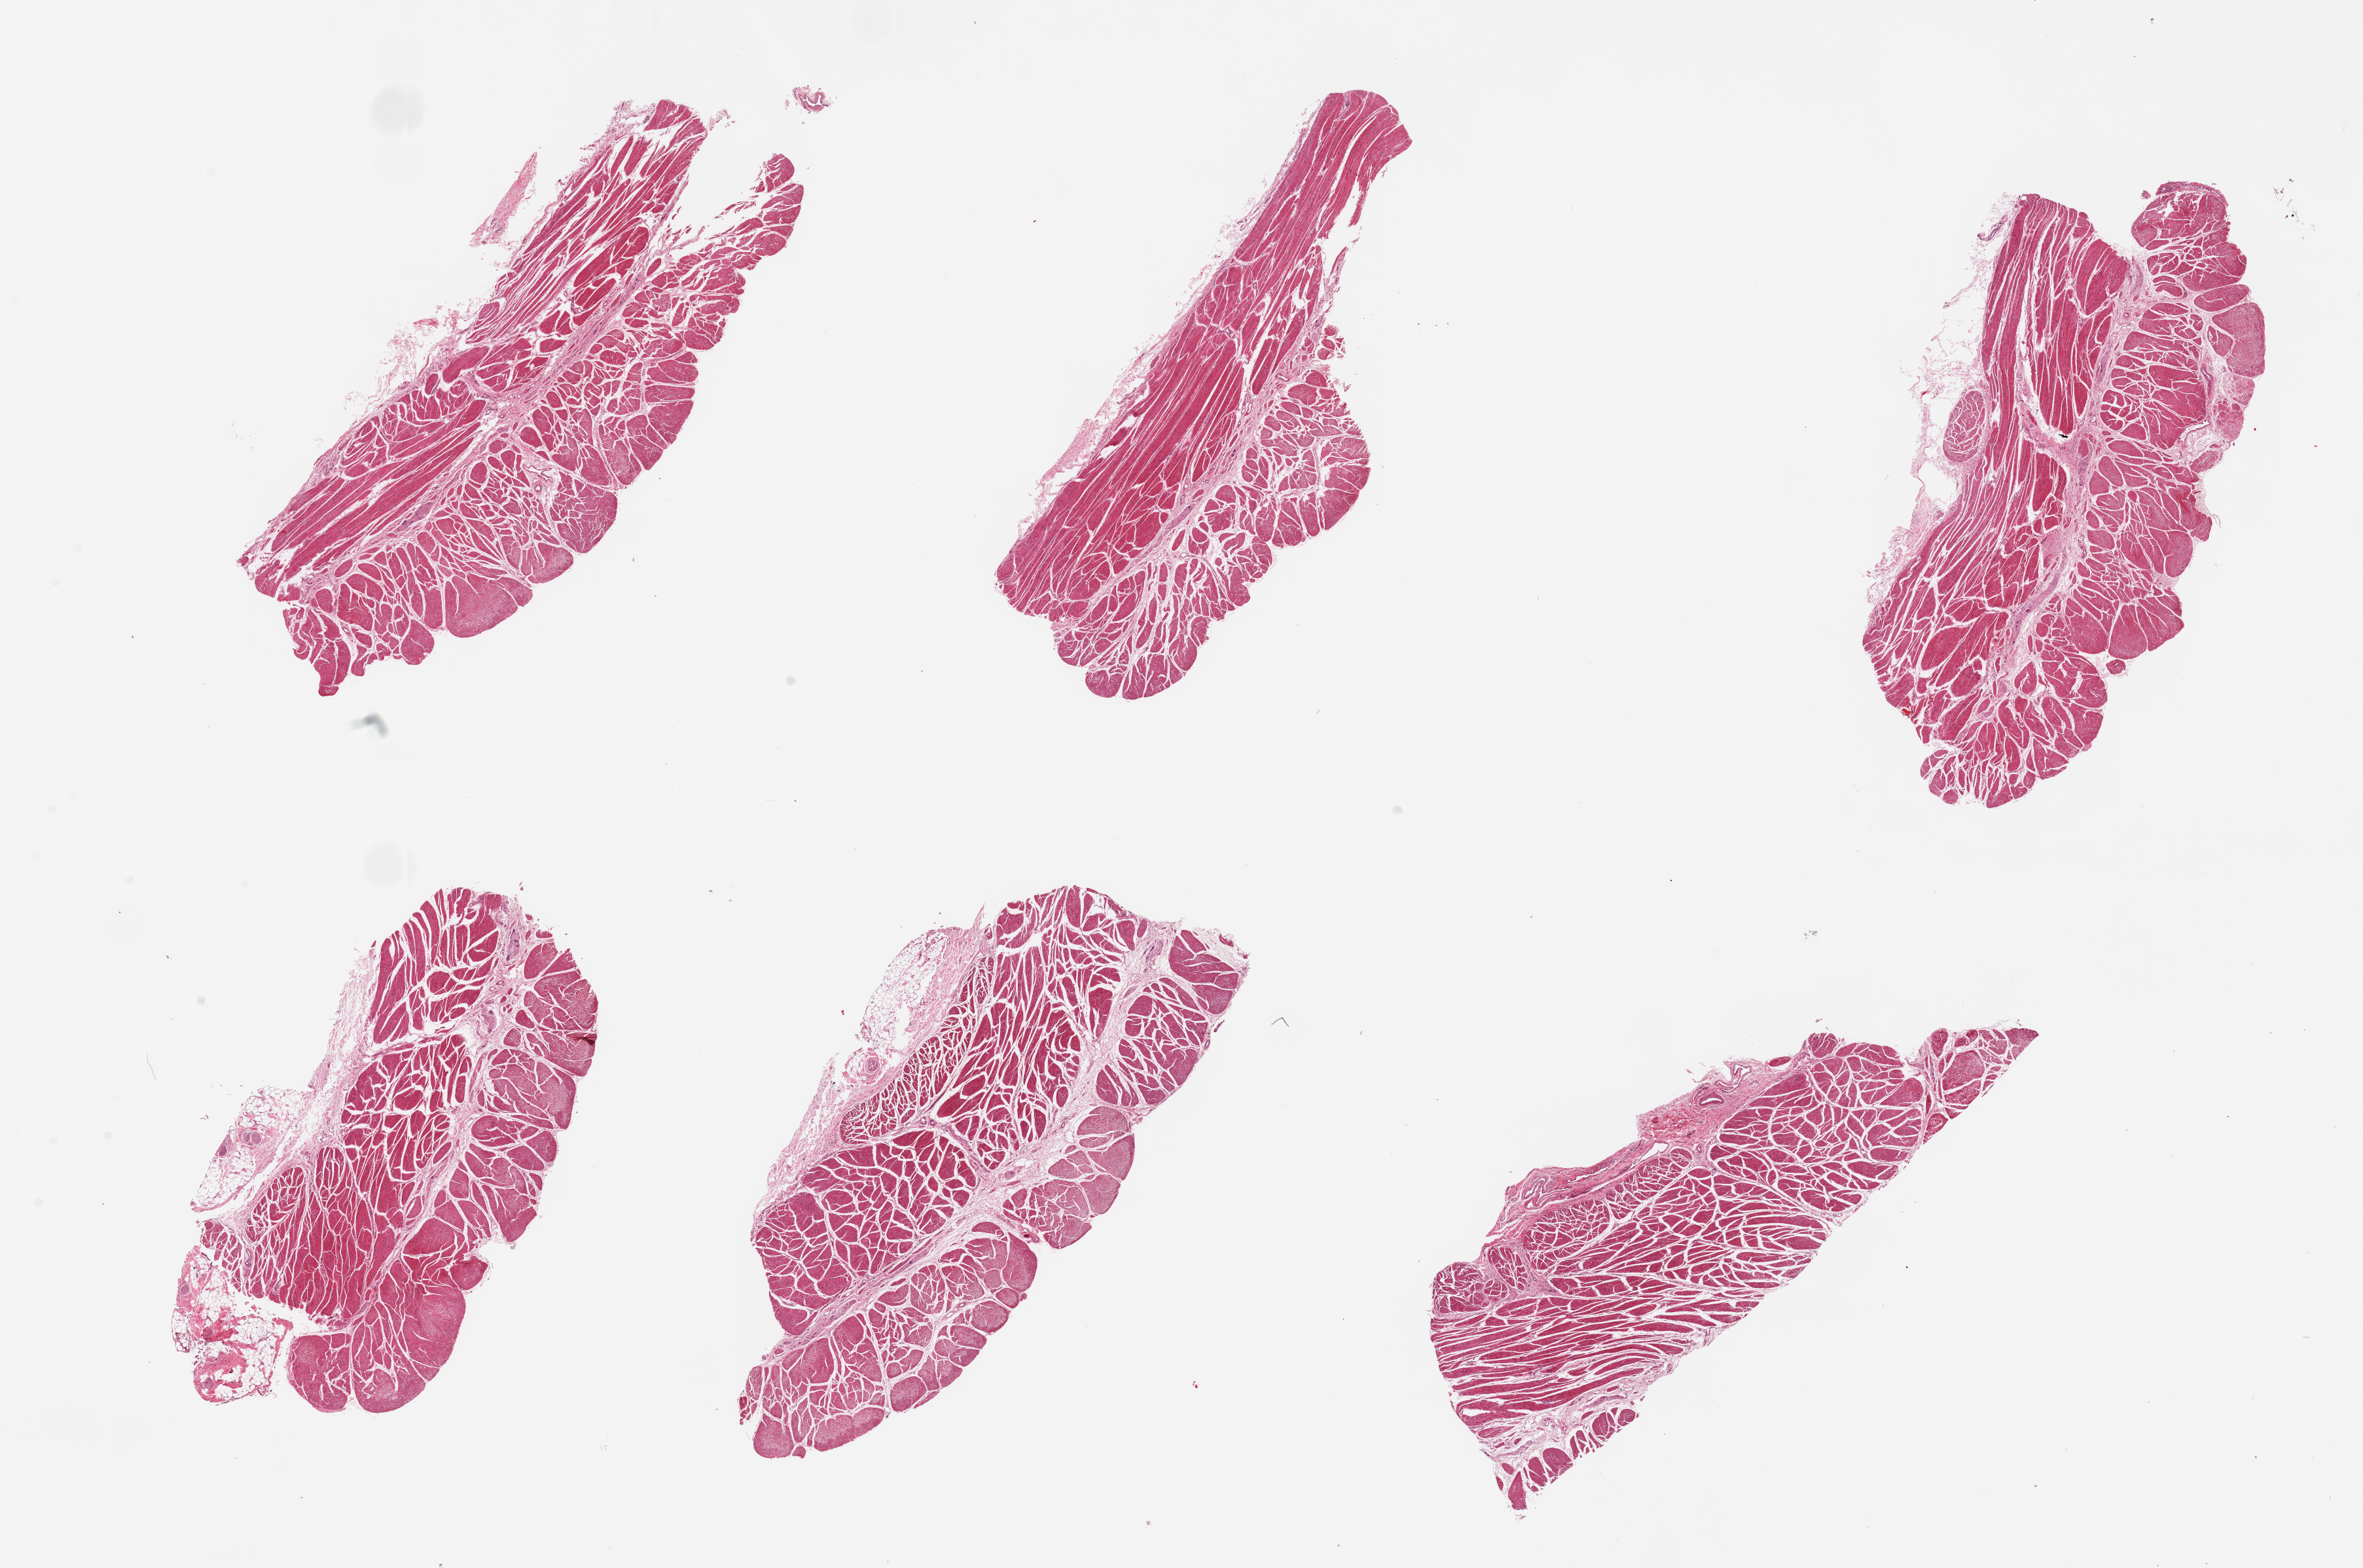
Whole-slide image, hematoxylin and eosin (H&E) stain, low-resolution overview of the scanned area, about 28.5 x 18.9 mm (slide scanned at 20x); PAXgene-fixed paraffin-embedded (PFPE) section; target tissue: esophageal muscle; tissue donor sample.
Review note (as recorded): 6 pieces. Well trimmed muscularis.